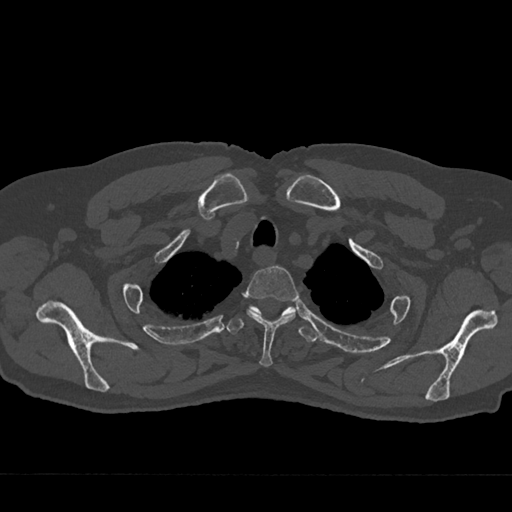
CT including the spine, one axial slice. Slice 597 of 797 in the series (ordered by position). Reconstruction kernel Br40s/3. Bone window (W 1800 / L 400 HU). 0.5 mm slice thickness. 512 × 512 image matrix, field of view 377 × 377 mm. Patient: male, 75 years. From the clinical record (not read from this slice): primary cancer: renal; vertebrae with lytic lesions (as recorded): T4.
Structures marked on this image (semi-automatically segmented with operator editing):
- T2 vertebra: bounding box (x1, y1, x2, y2) in pixels: (243, 266, 298, 367)
- T3 vertebra: (226, 306, 318, 342)